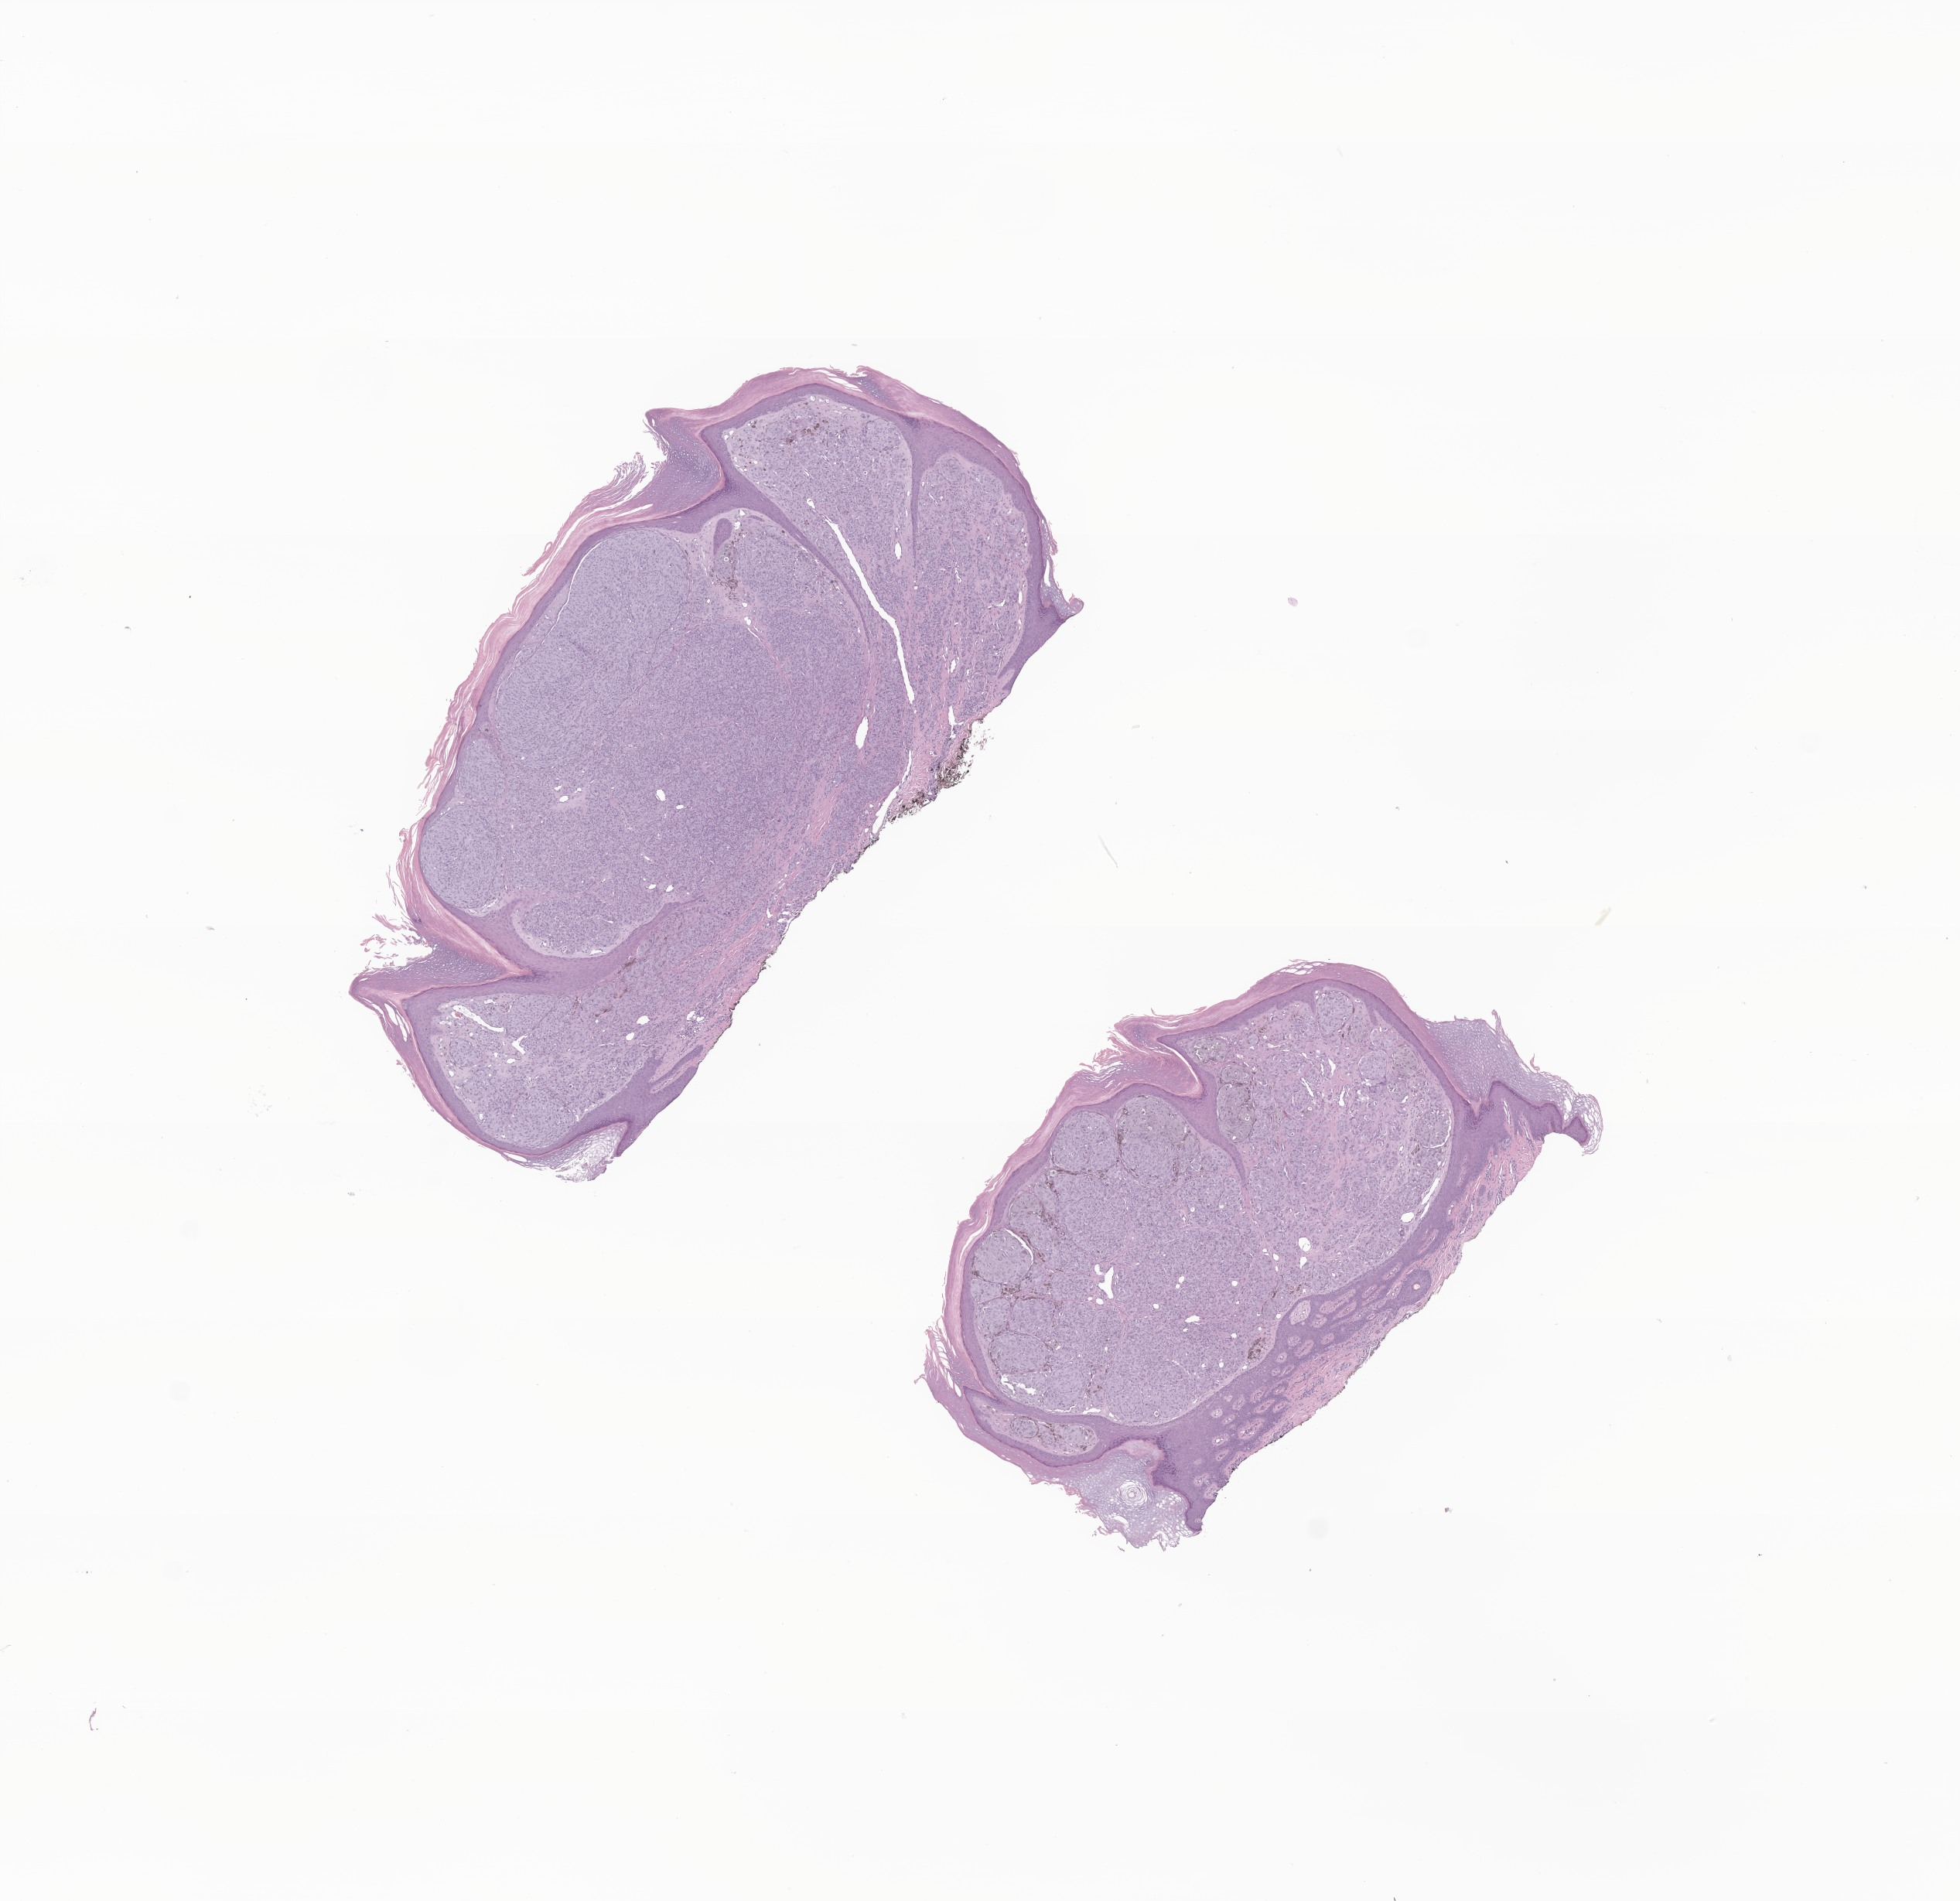
Whole-slide image, hematoxylin and eosin (H&E) stain of tumor tissue from the skin of upper limb — low-resolution overview of the scanned area, about 10.7 x 10.4 mm; FFPE section. Female patient, age 142 months (11 years 10 months).
Diagnosis: Malignant melanoma, NOS.